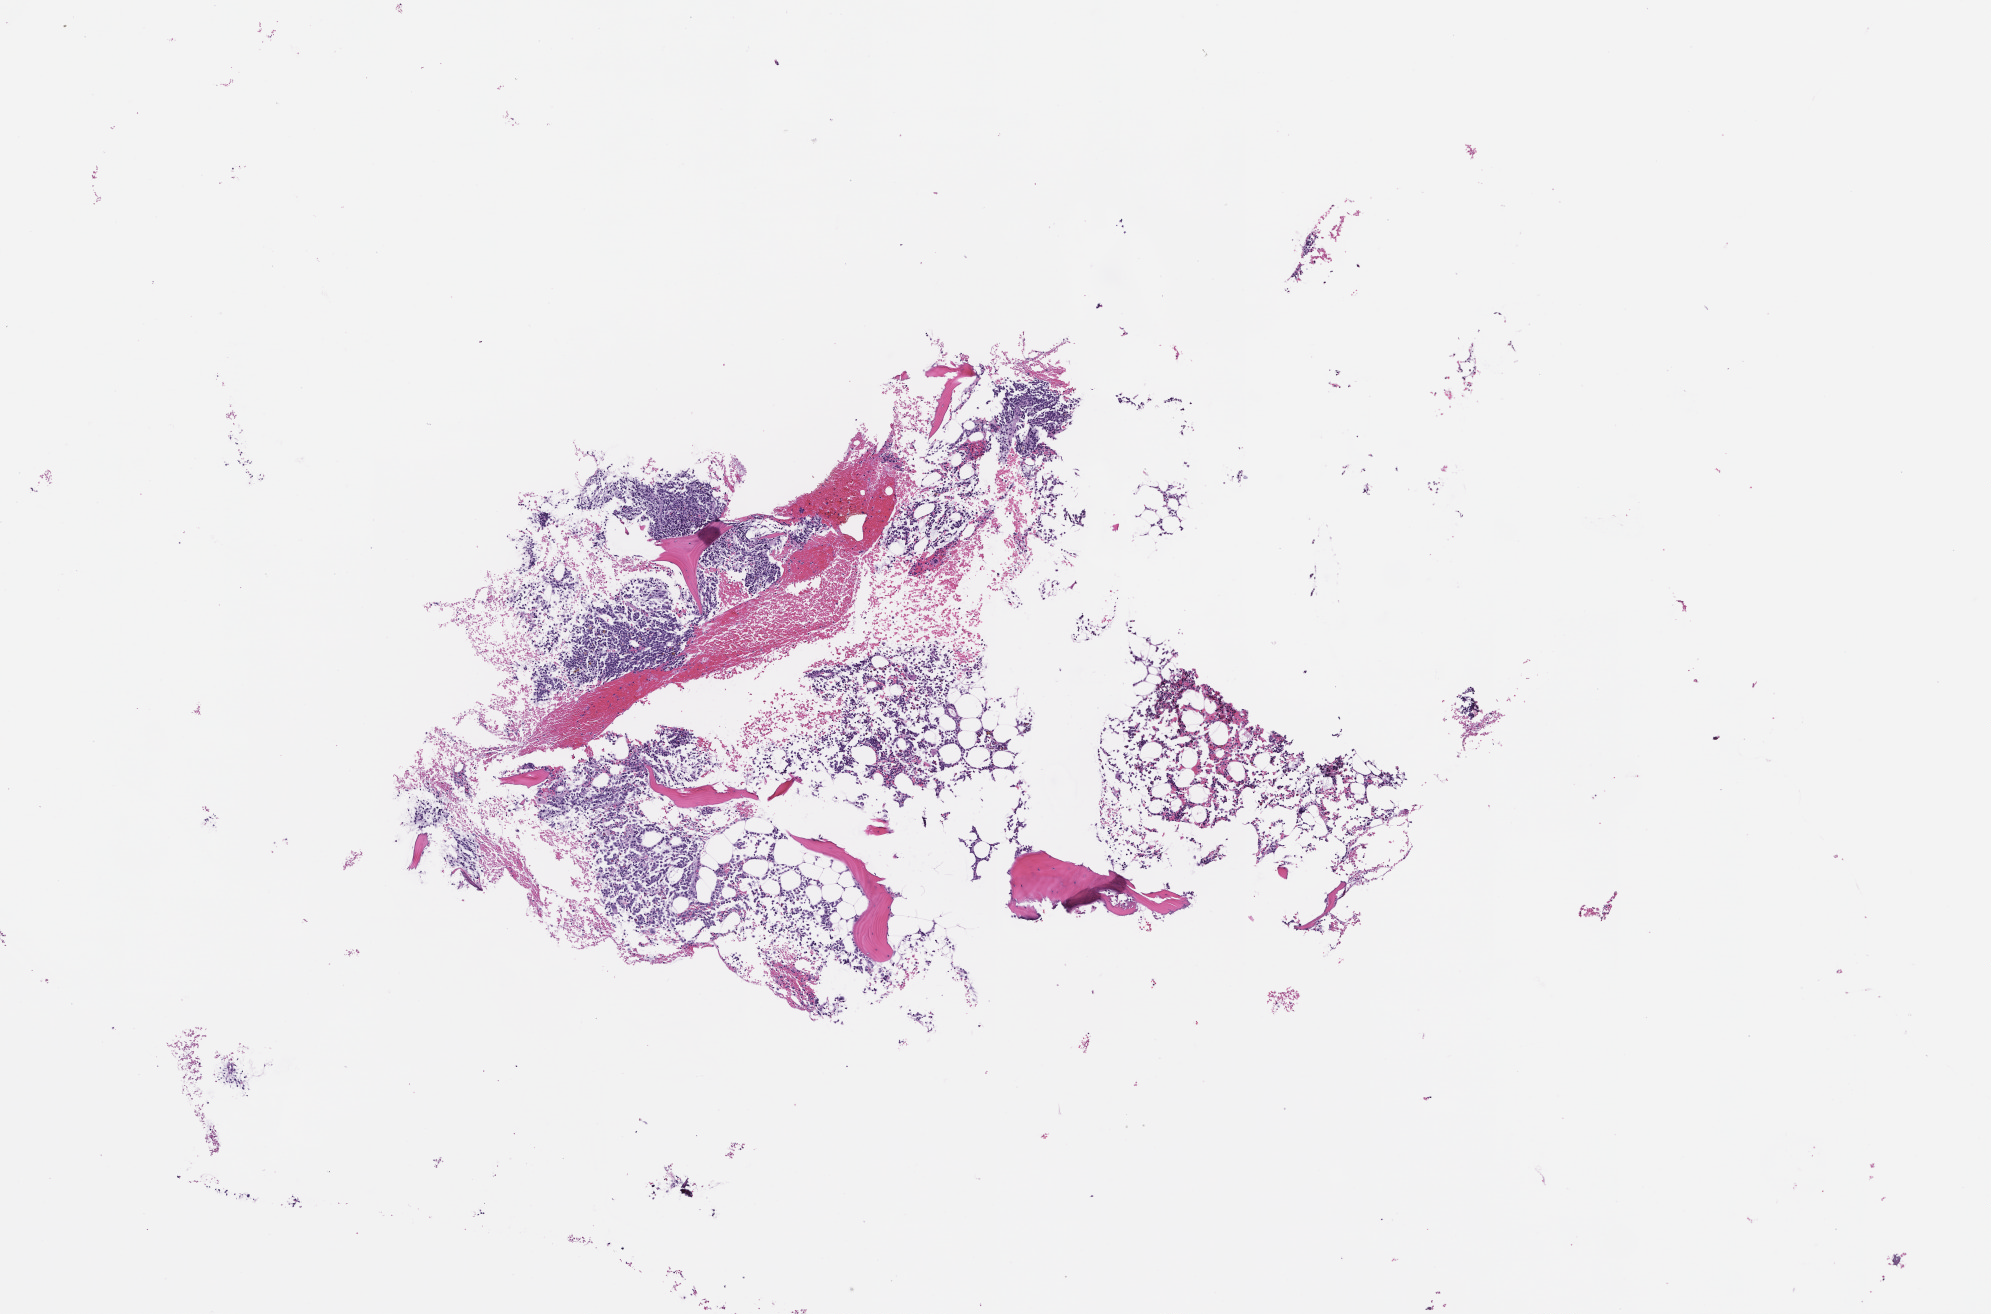
Whole-slide image, H&E stain, a low-resolution overview of the entire scanned area, about 8.0 x 5.3 mm; formalin-fixed paraffin-embedded section; site: bone marrow; collected at baseline (before treatment). Male patient.
* this section: primary tumour tissue
* diagnosis: Plasma Cell Myeloma